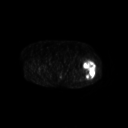
FDG PET of an extremity soft-tissue mass (from a PET/CT study), one axial slice; 128 × 128 image matrix, field of view 700 × 700 mm. Female patient, age 62 years. Case-level facts recorded for this patient, not image findings: histological type: undifferentiated – high grade; grade: high; site of the primary tumour: left thigh.
Structures marked on this image (expert contour drawn on MRI and transferred to this co-registered scan by the dataset authors):
- gross tumour volume including surrounding oedema: bounding box (x1, y1, x2, y2) in pixels: (82, 60, 96, 80)
- gross tumour volume (mass): (82, 61, 95, 80)